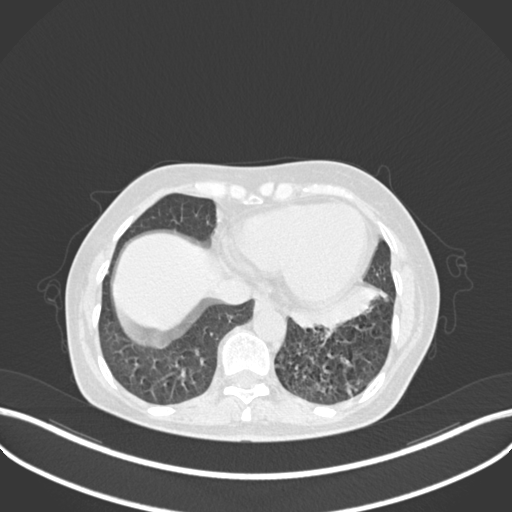
Chest CT, one axial slice; slice 70 of 270 in the series (ordered by position); reconstruction kernel B30f; 120 kVp; lung window (W 1500 / L -600 HU); 1 mm slice thickness; 512 × 512 image matrix, field of view 400 × 400 mm. Patient: female, 63 years. Case-level facts recorded for this patient, not image findings: clinical TNM (as recorded): T1b N0 M0; histopathological grade: G2-3.
Annotated regions visible in this slice (rectangle marked by the reading radiologist):
- lung tumour (recorded histology: adenocarcinoma): bounding box <290,284,391,338> (left, top, right, bottom; pixels)